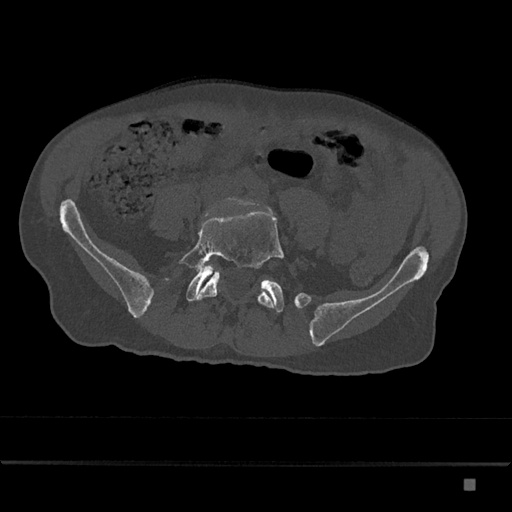
CT including the spine, one axial slice. Position 269 of 797 along the scan axis. 120 kVp. Bone window (W 1800 / L 400 HU). 0.5 mm slice thickness. 512 × 512 image matrix, field of view 390 × 390 mm. Patient: male, 72 years. Case-level facts recorded for this patient, not image findings: primary cancer: prostate.
Annotated regions visible in this slice (semi-automatically segmented with operator editing):
- L5 vertebra: bounding box (x1, y1, x2, y2) in pixels: (178, 211, 284, 308)